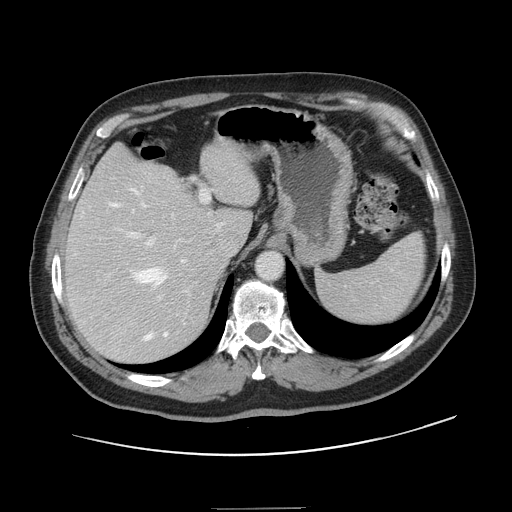
Contrast-enhanced abdominal CT, one axial slice. Position 102 of 143 along the scan axis. 120 kVp. Intravenous contrast given. Soft-tissue window (W 400 / L 40 HU). 2.5 mm slice thickness. 512 × 512 image matrix, field of view 402 × 402 mm. Male patient, age 62 years. From the clinical record (not read from this slice): diagnosis: colorectal cancer liver metastases, imaged before liver resection; multiple liver metastases: yes; largest metastasis: 2.7 cm; disease in both lobes: no.
Structures marked on this image (outlined manually by an expert reader):
- hepatic veins: box from (x=109, y=189) to (x=187, y=340) px
- liver: (x=66, y=144)–(x=259, y=363)
- planned liver remnant (the part of the liver to remain after resection): (x=67, y=144)–(x=258, y=265)
- portal vein (with intrahepatic branches): (x=118, y=190)–(x=210, y=334)